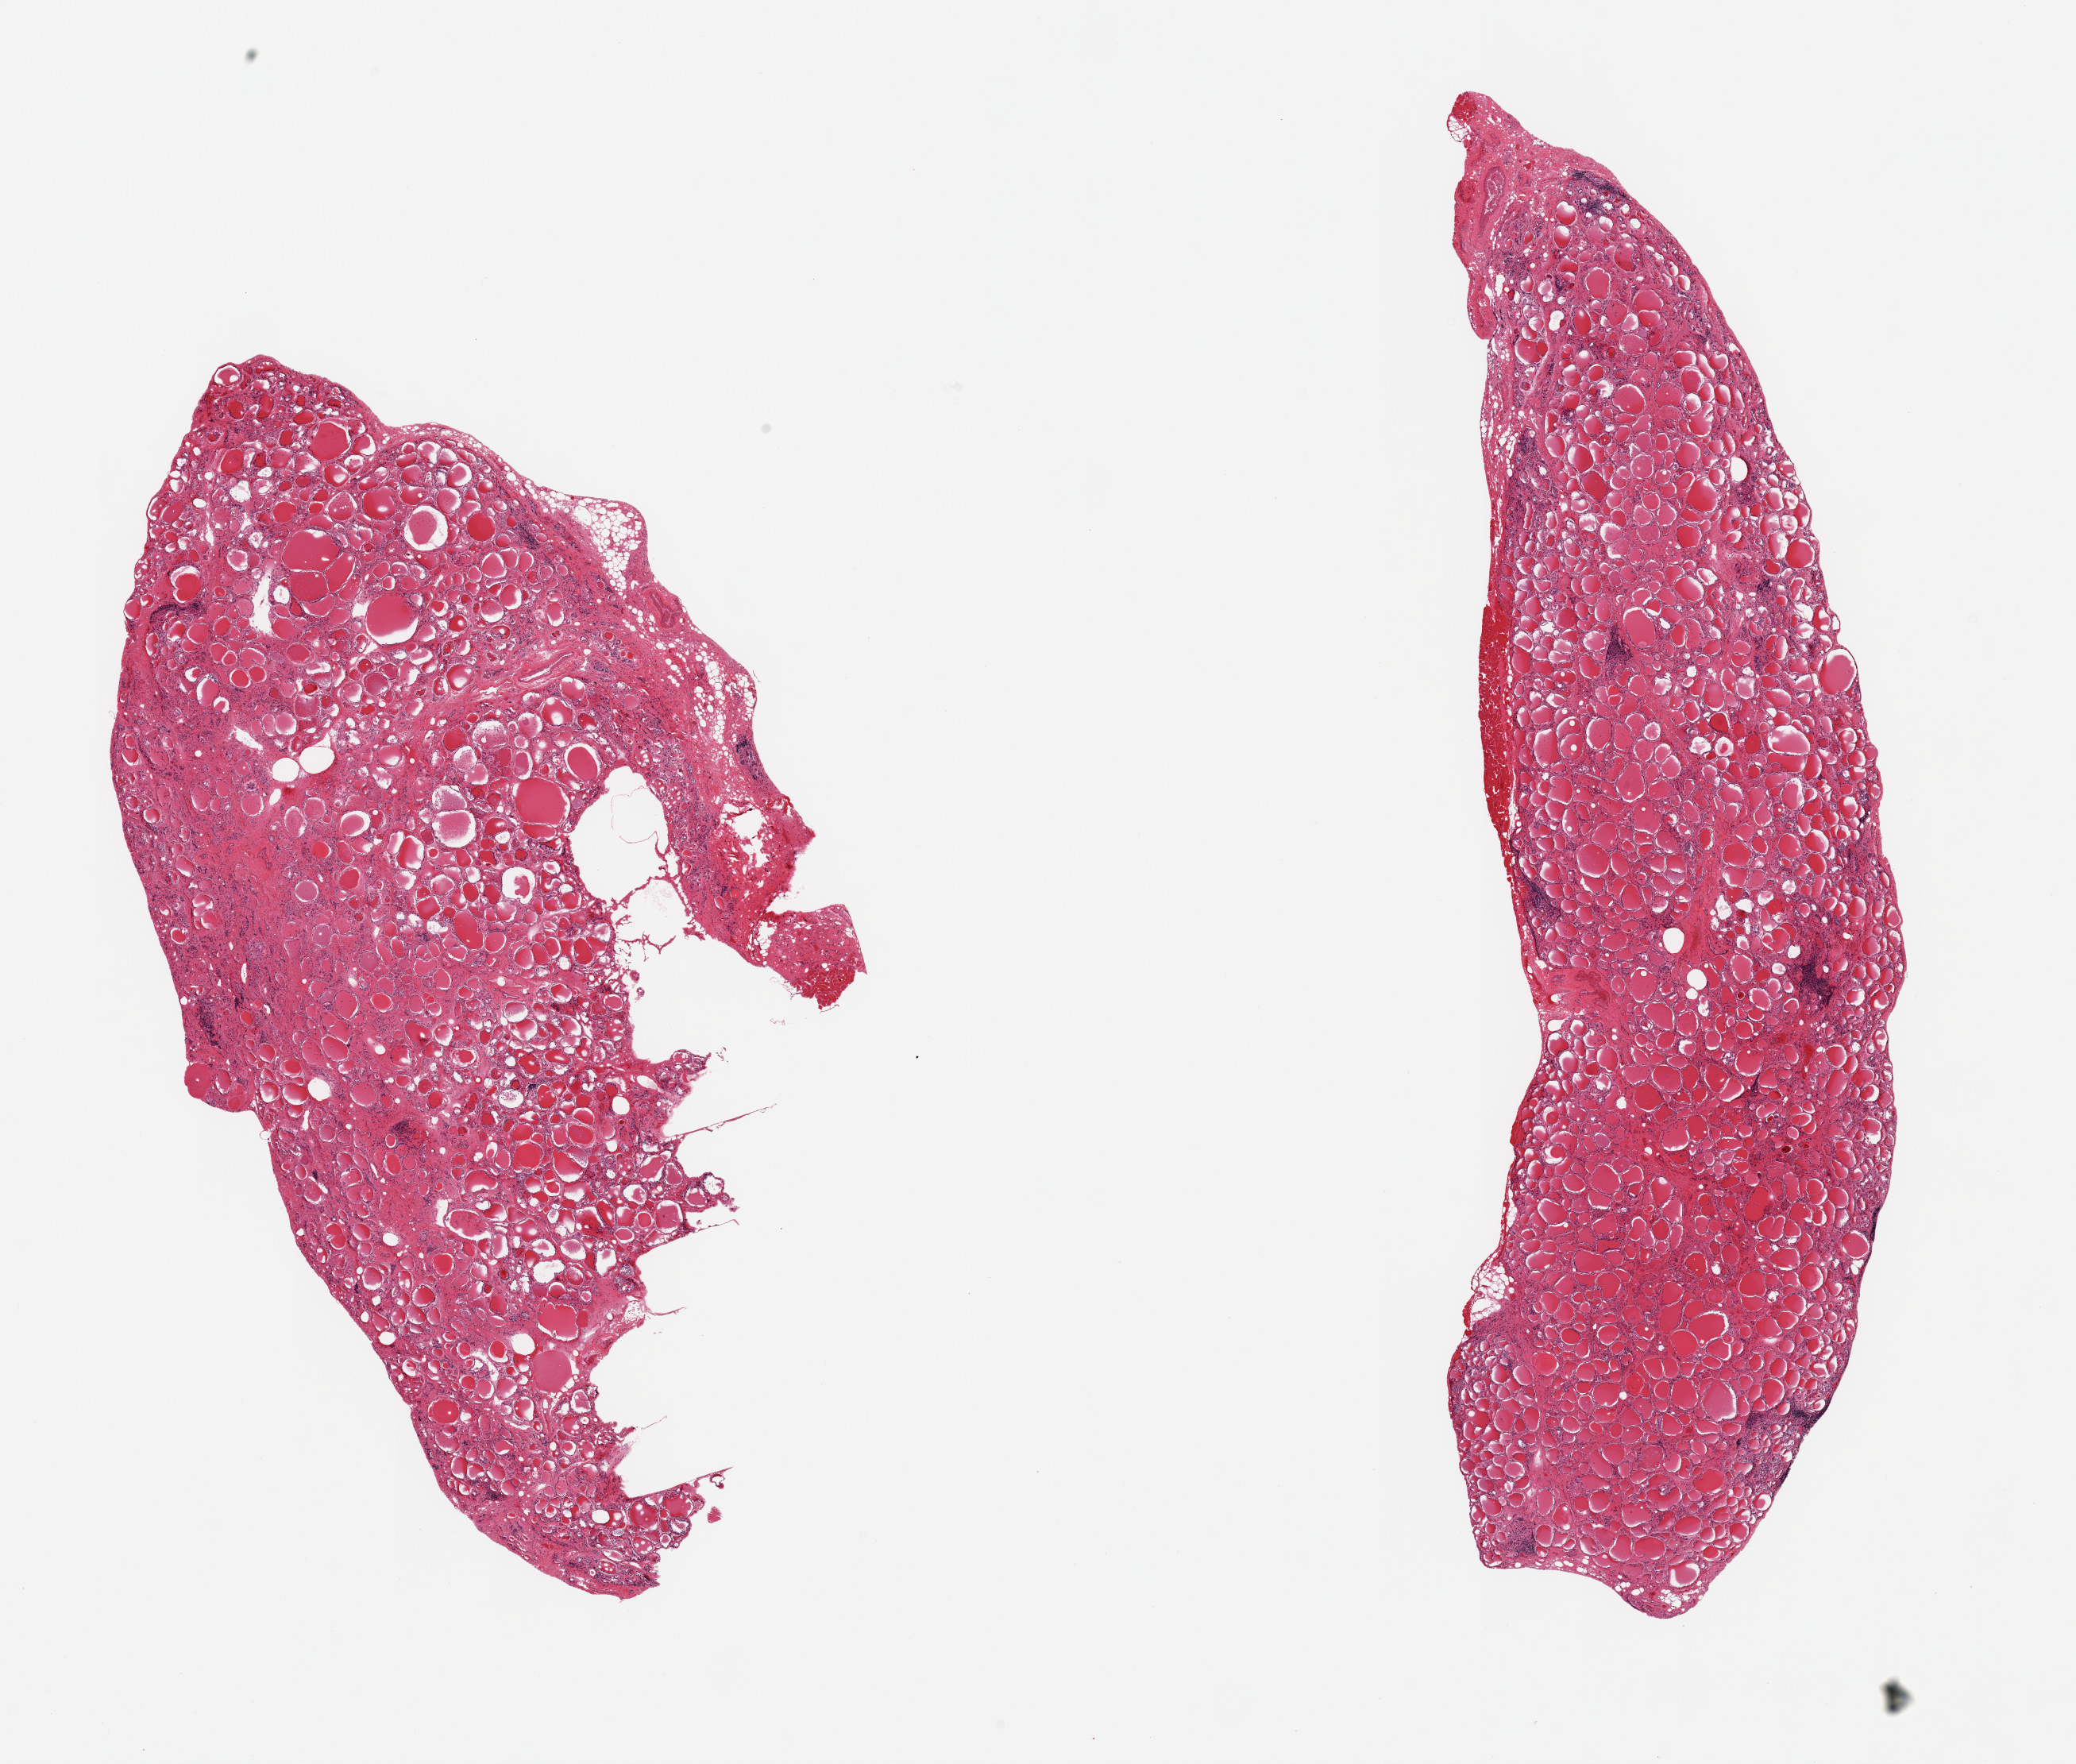
Digitized hematoxylin and eosin (H&E)-stained section, whole scanned area (about 20.7 x 17.6 mm) shown as a low-resolution overview. PAXgene-fixed paraffin-embedded (PFPE) section. Section of thyroid (target tissue). Donor tissue sample. Donor sex: female.
Reviewer comment on this tissue sample: 2 pieces; several foci of lymphocytes, possible Hashimoto.